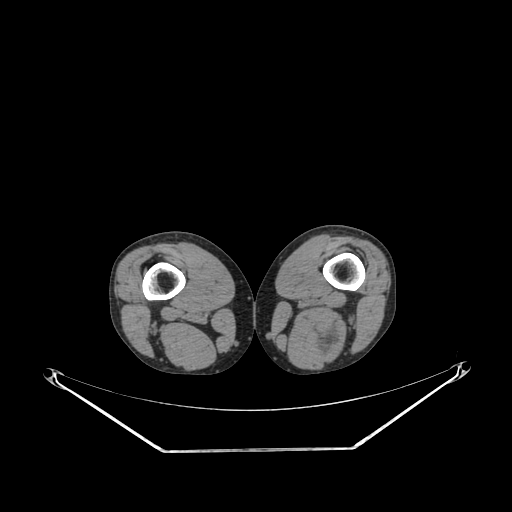
CT of an extremity soft-tissue mass (from a PET/CT study), one axial slice. Slice 202 of 267 in the series (ordered by position). 140 kVp. Soft-tissue window (W 400 / L 40 HU). 3.75 mm slice thickness. 512 × 512 image matrix, field of view 500 × 500 mm. Male patient. From the clinical record (not read from this slice): histological type: synovial sarcoma; site of the primary tumour: left poplietal fossa.
Outlined on this slice (expert contour drawn on MRI and transferred to this co-registered scan by the dataset authors):
- gross tumour volume (mass): bounding box (x1, y1, x2, y2) in pixels: (313, 329, 336, 353)